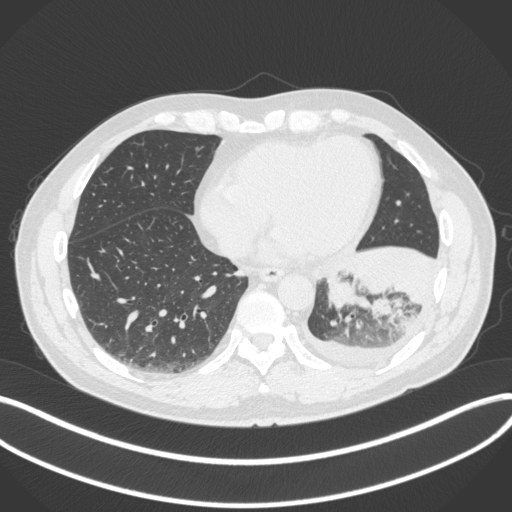
Chest CT, one axial slice; position 112 of 350 along the scan axis; reconstruction kernel B31f; 120 kVp; lung window (W 1500 / L -600 HU); 1 mm slice thickness; 512 × 512 image matrix, field of view 400 × 400 mm. Patient: male, 58 years. From the clinical record (not read from this slice): clinical TNM (as recorded): T3 N1 M1b.
Structures marked on this image (rectangle marked by the reading radiologist):
- lung tumour (recorded histology: small cell carcinoma): box from (x=325, y=264) to (x=374, y=314) px